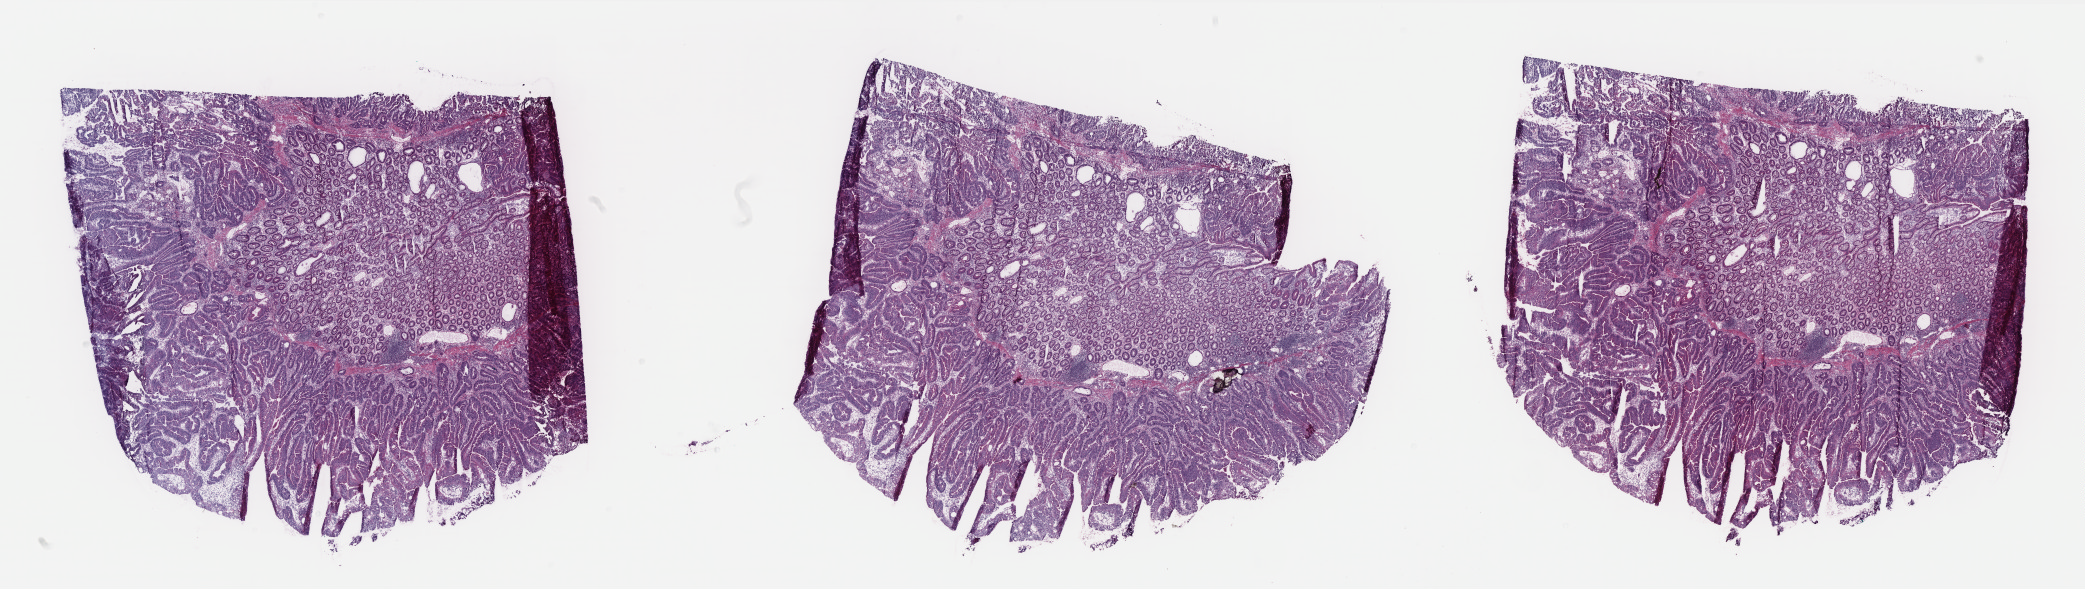
Whole-slide histology image, H&E-stained — shown as a low-resolution overview of the whole scanned area (about 33.4 x 9.4 mm, acquisition: 40x scan), frozen section, colon, primary tumour sample. Male patient; age at initial diagnosis 67 years. Pathologist review of this section (percent, as recorded): tumour cells 55%, tumour nuclei 65%, normal cells 35%, stromal cells 8%, necrosis 2%. Infiltration values recorded for this section: lymphocyte infiltration 18%, monocyte infiltration 0%, neutrophil infiltration 0%.
Histologic diagnosis: Adenocarcinoma, NOS. AJCC pathologic stage: II (5th edition). Lymph nodes positive (case pathology): 0 of 27 examined. TNM: T3 N0 M0.